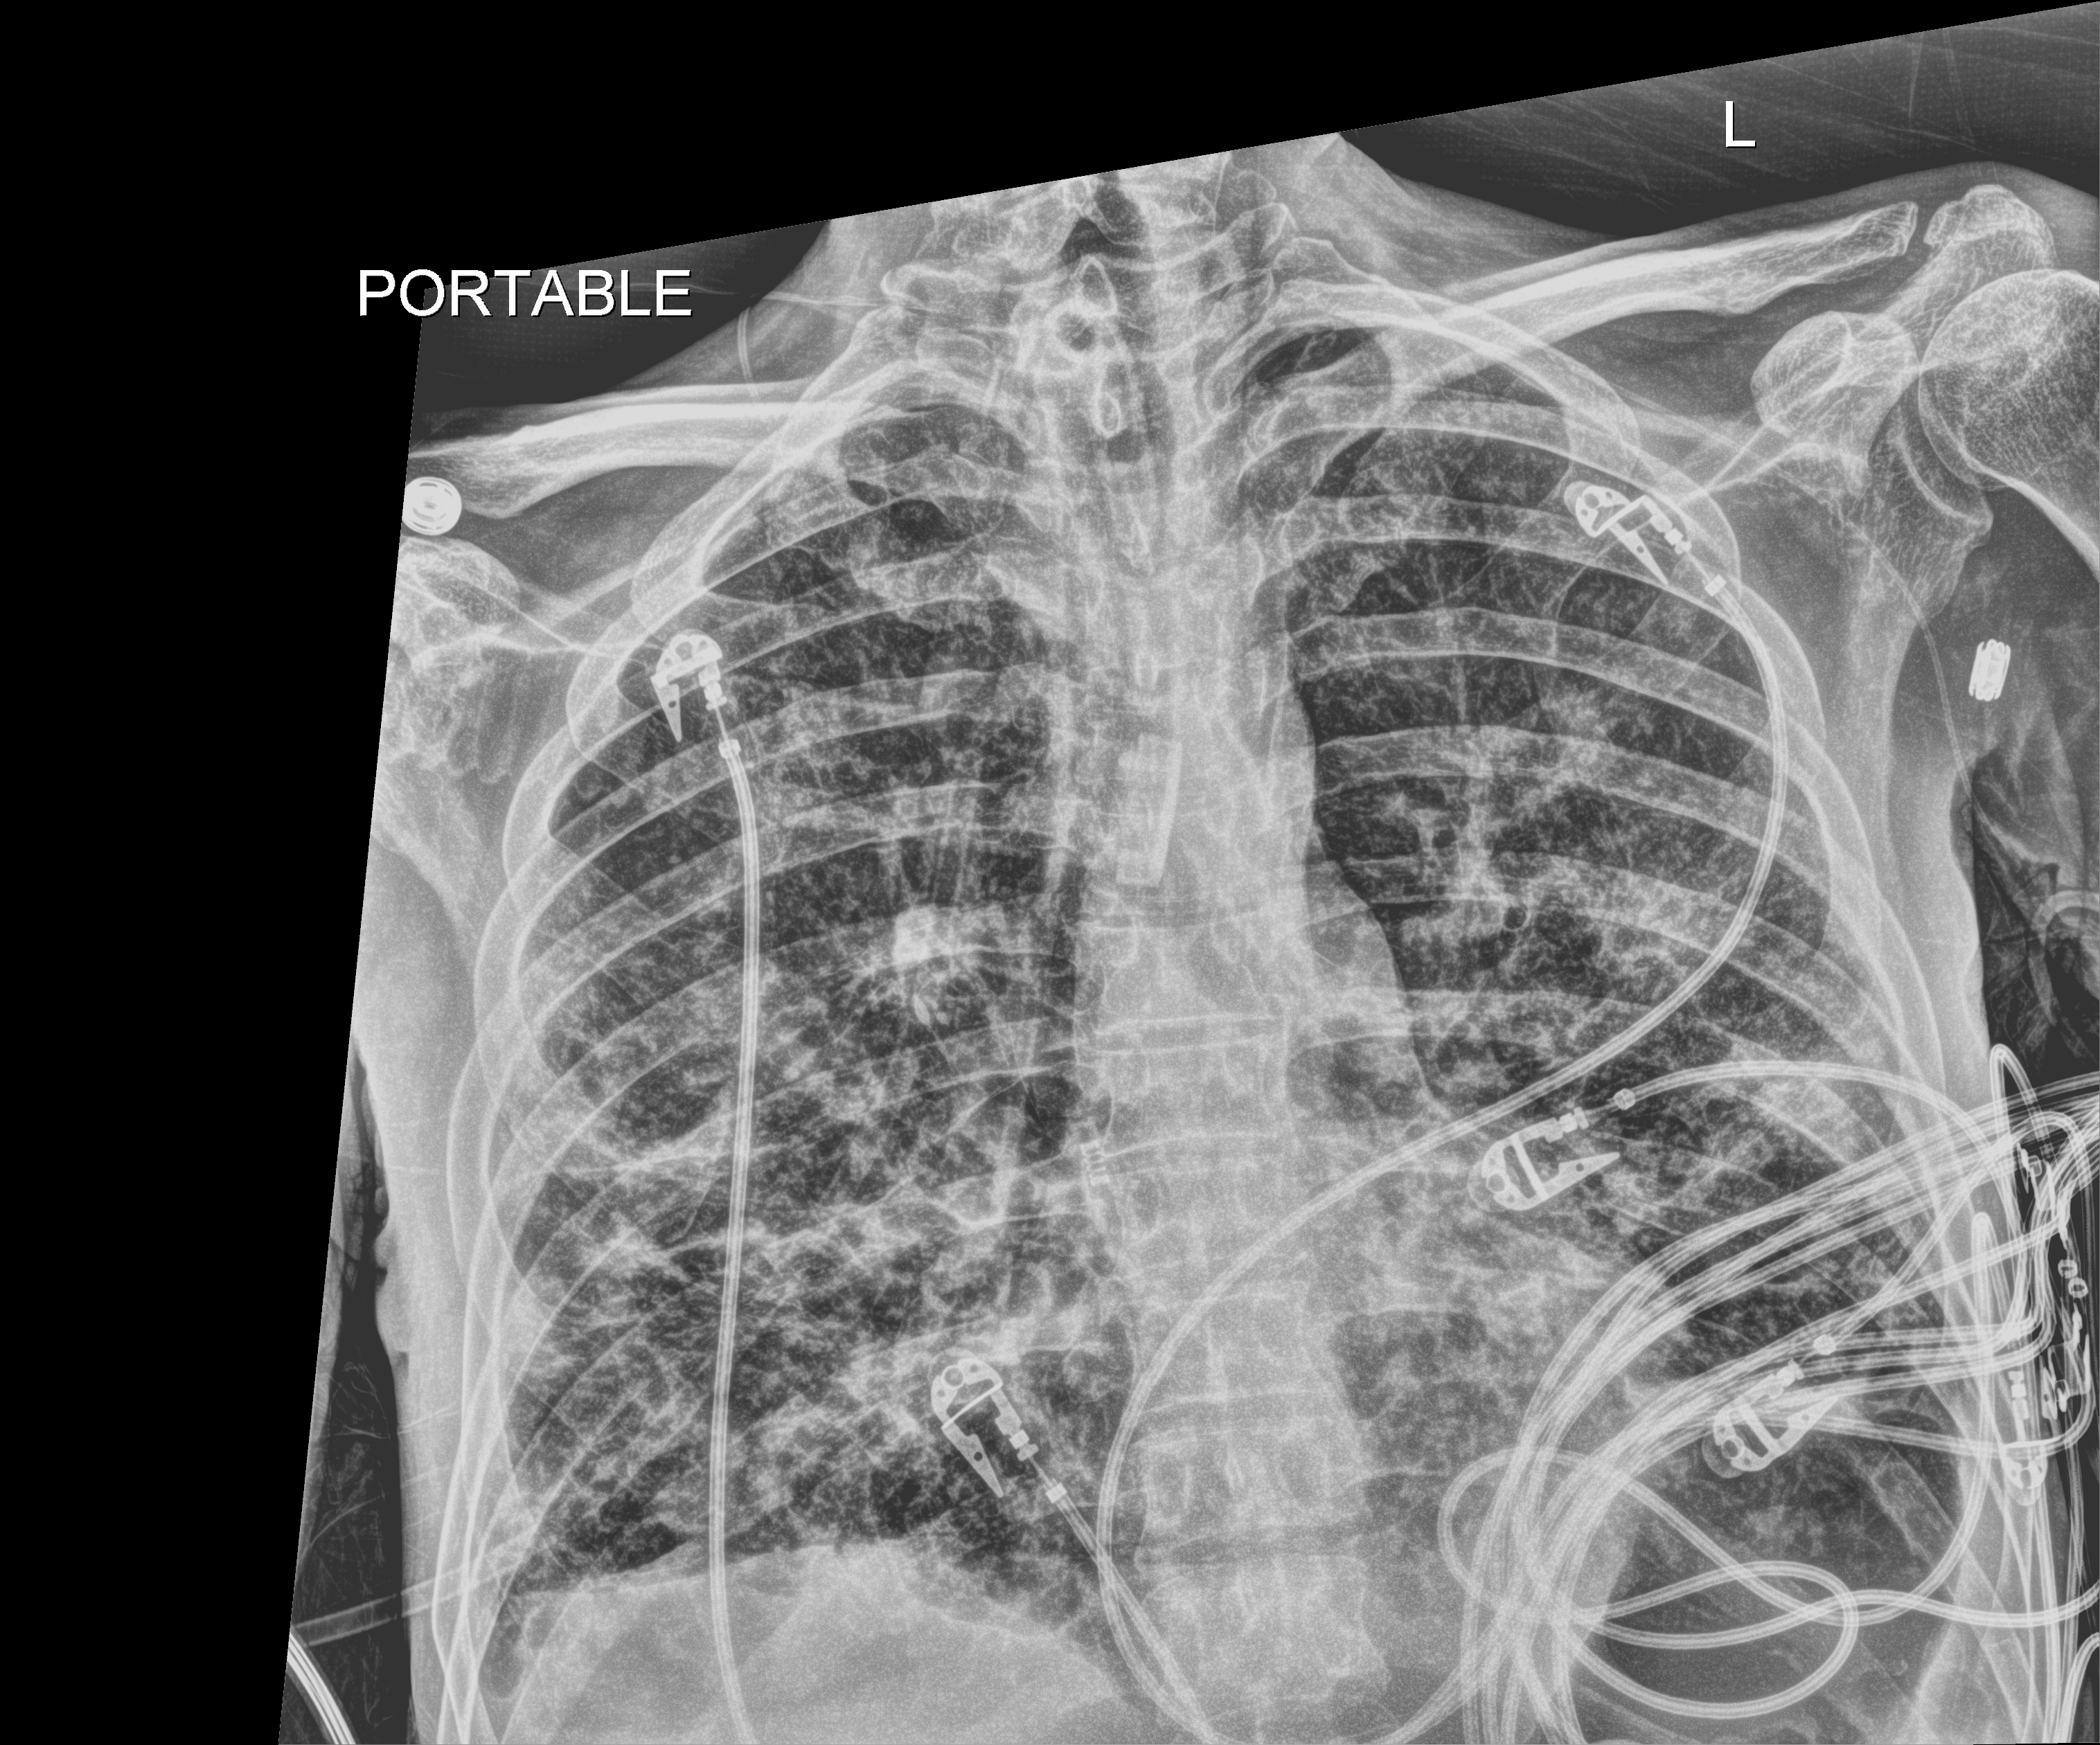
Chest radiograph. Male patient hospitalised with COVID-19, age 18–59 years.
From the hospital-stay record, not from the radiograph (when in the stay this image was taken is not recorded): mechanically ventilated during this hospital stay: yes; admitted to intensive care during this hospital stay: yes; length of hospital stay: 96 days.